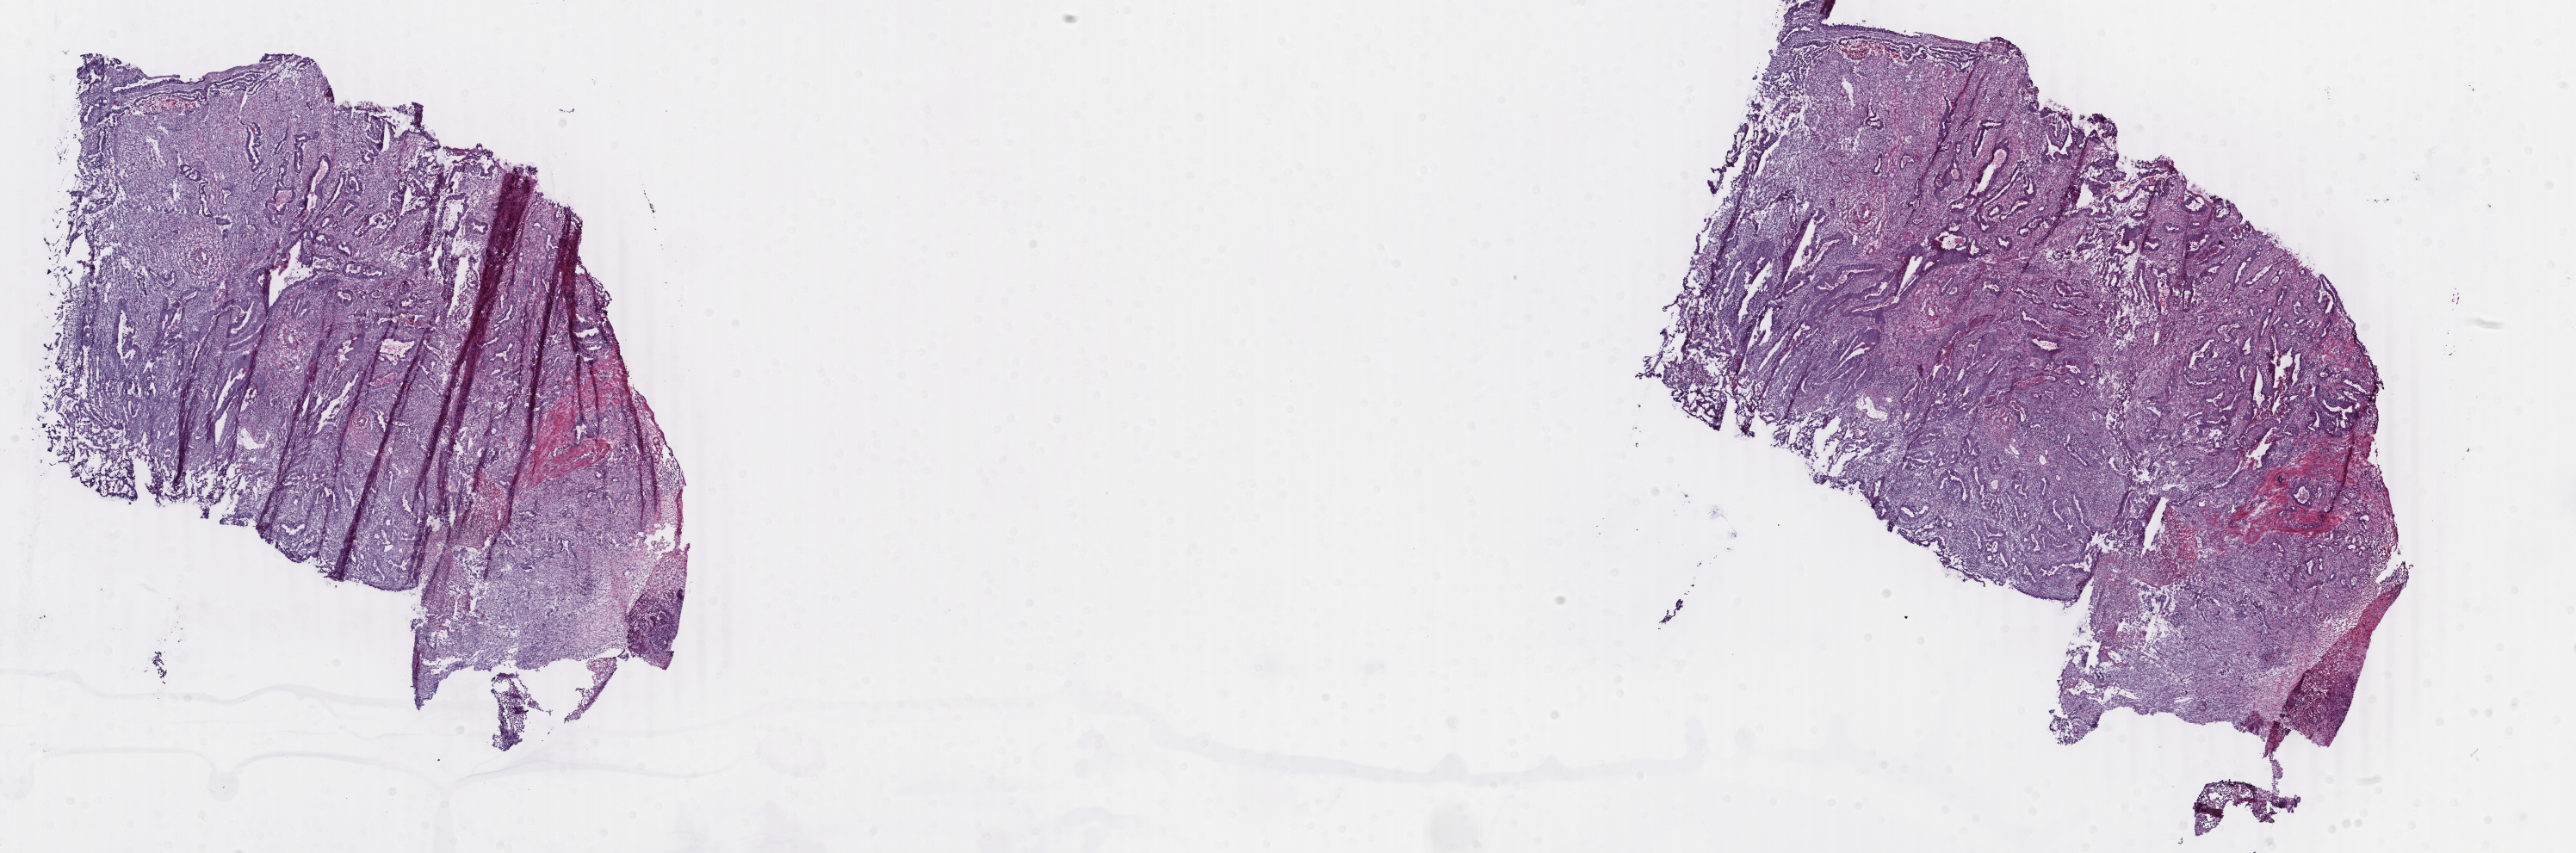
Whole-slide histology image, Hematoxylin and eosin (H&E) stained — a low-resolution overview of the entire scanned area, about 23.8 x 7.9 mm (from a 40x scan), frozen section, primary tumour sample from the colon. Patient: female, age at initial diagnosis 74 years. Composition of this section per pathologist review: tumour cells 80%, tumour nuclei 70%, normal cells 0%, stromal cells 15%, necrosis 5%. Infiltration values recorded for this section: lymphocyte infiltration 14%, monocyte infiltration 2%, neutrophil infiltration 8%.
* histologic diagnosis: Adenocarcinoma, NOS (sigmoid colon)
* AJCC pathologic stage: IIIC